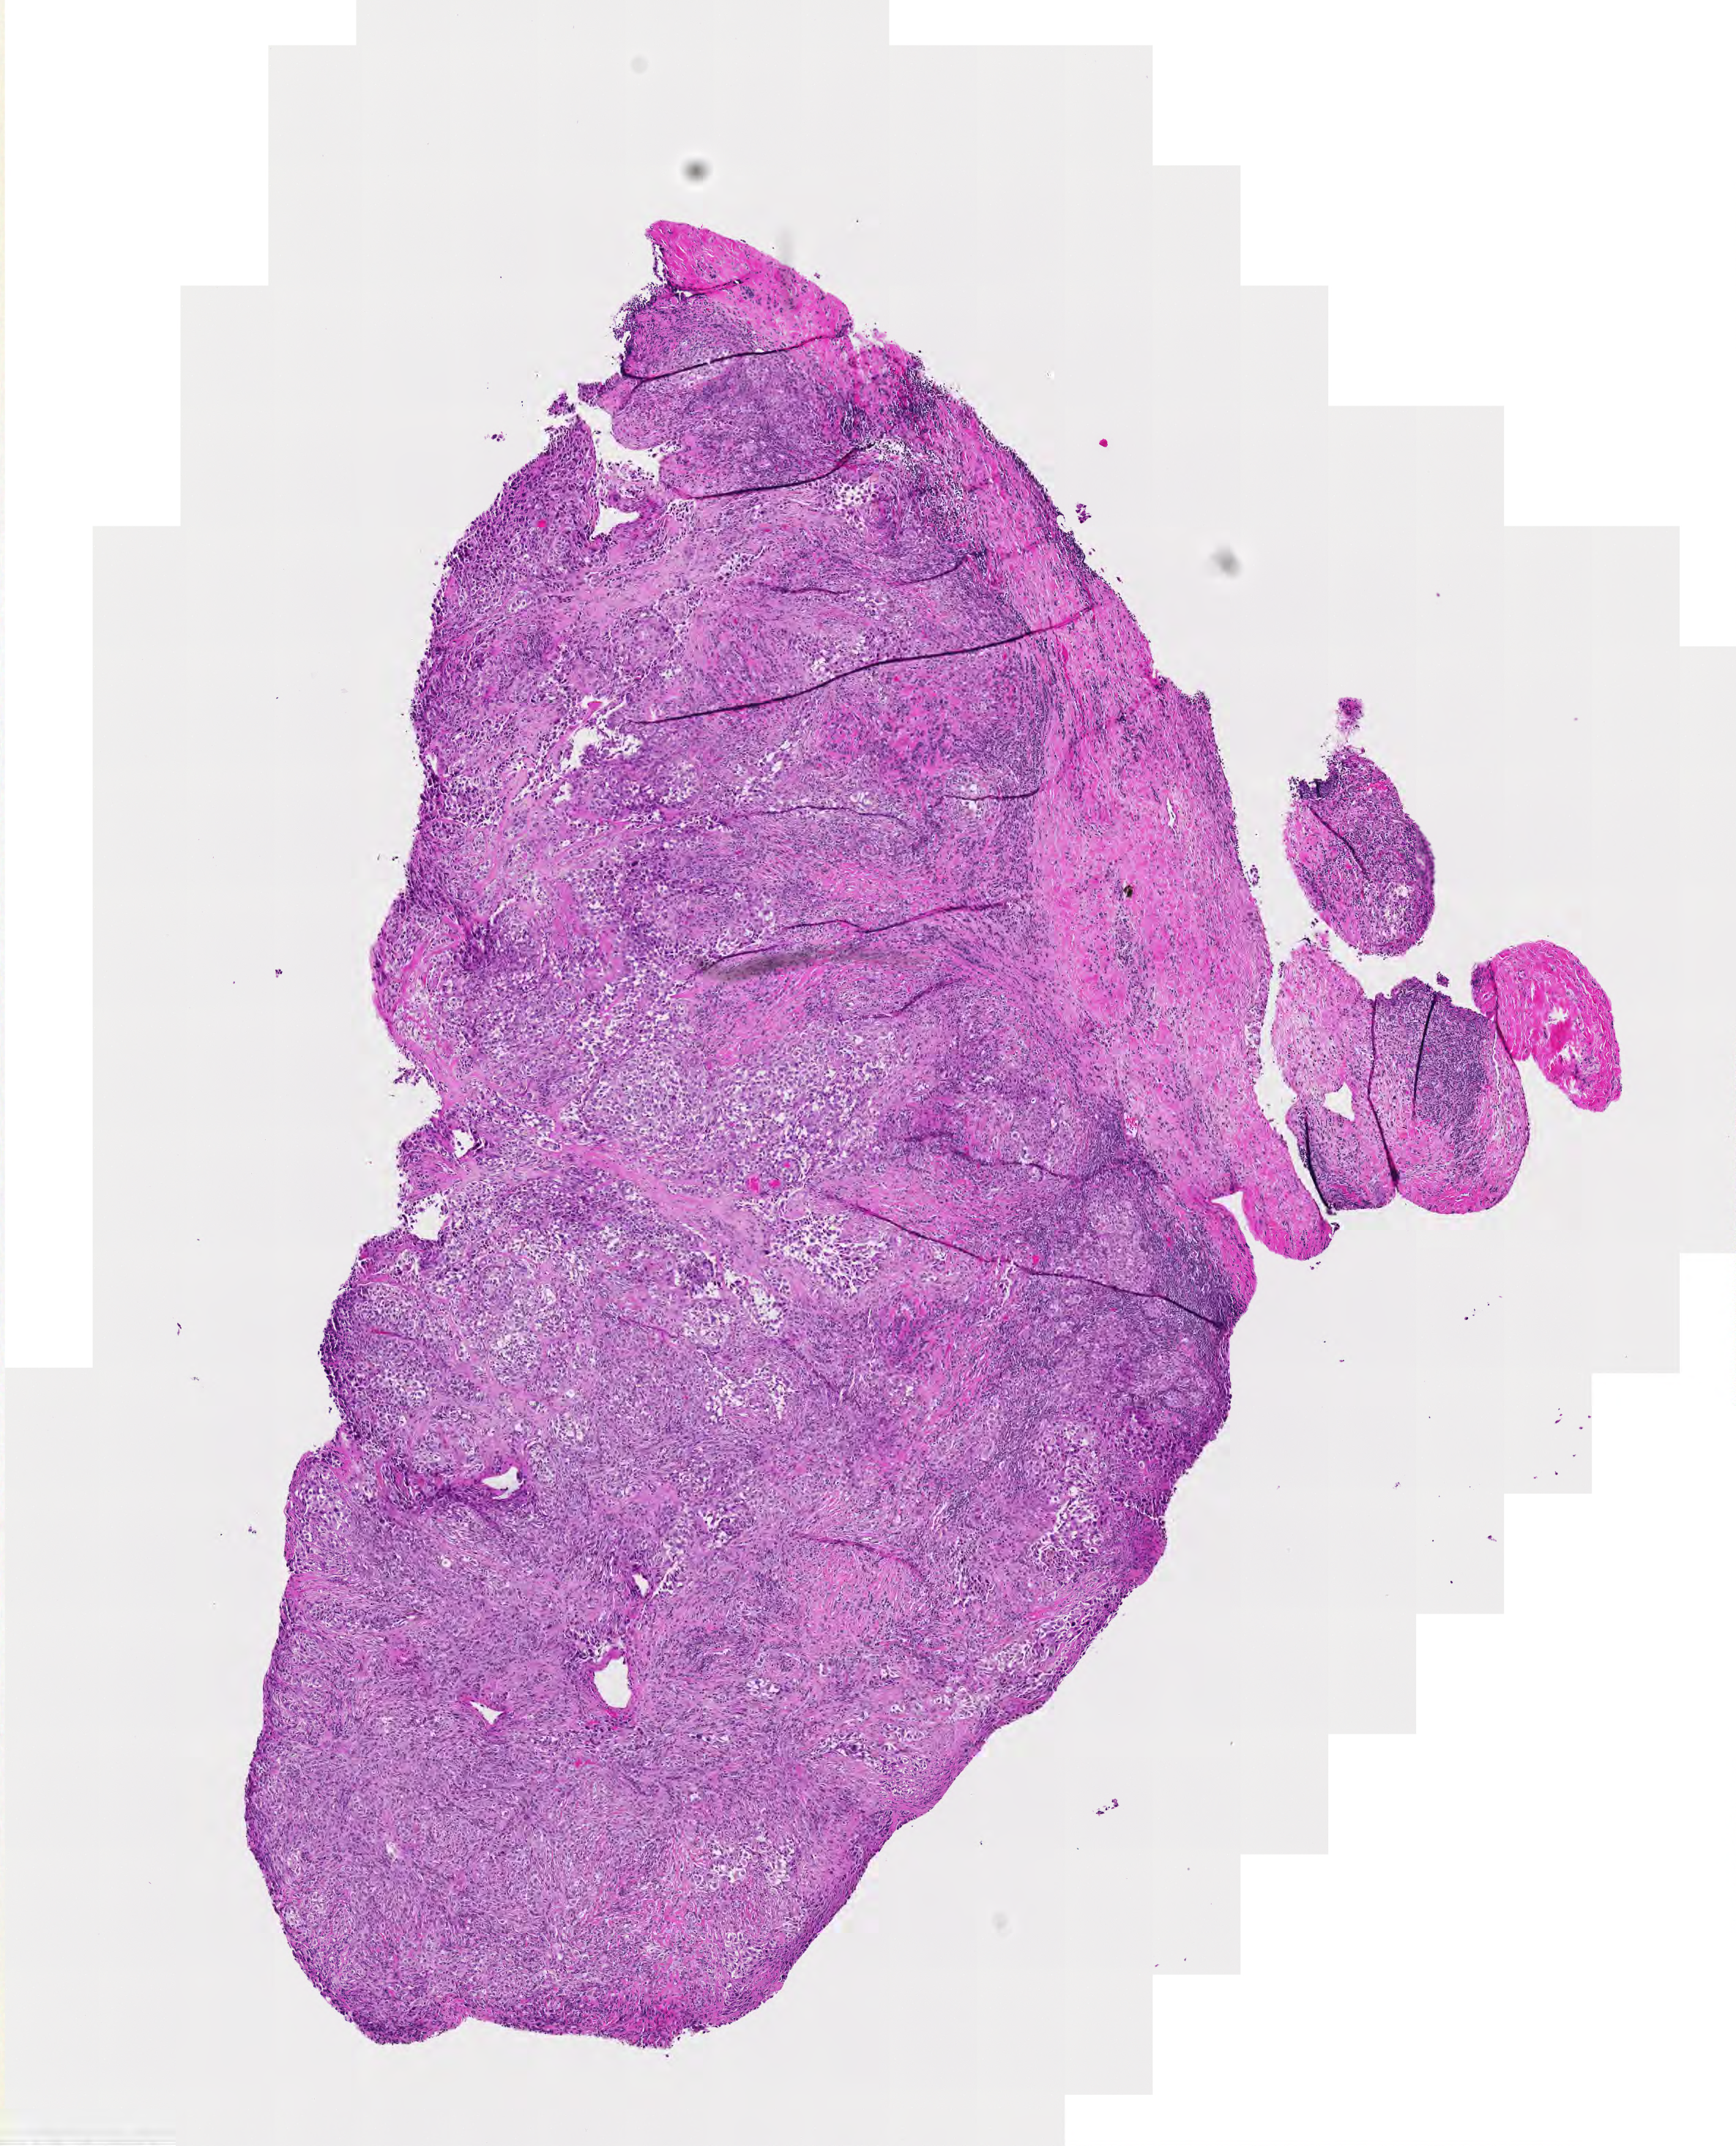
Digitized H&E-stained tissue section (whole slide) — shown as a low-resolution overview of the whole scanned area (about 6.1 x 7.6 mm, slide scanned at 20x), melanoma tumour tissue; sampled site not recorded. Patient: male, age 68 years.
Histologic diagnosis: Malignant melanoma, NOS. AJCC pathologic stage: 0.